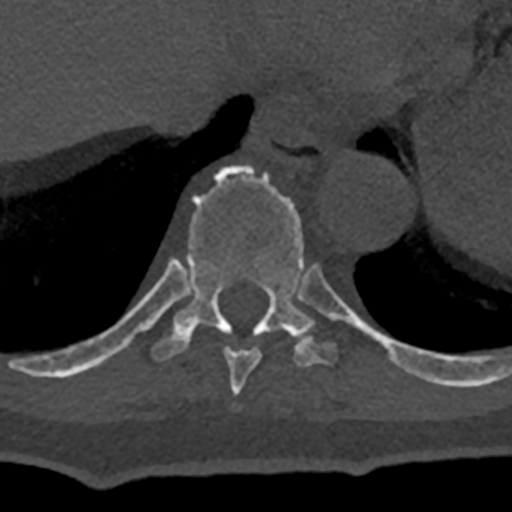
CT including the spine, one axial slice; position 620 of 797 along the scan axis; reconstruction kernel Br40s/3; 120 kVp; bone window (W 1800 / L 400 HU); 512 × 512 image matrix, field of view 160 × 160 mm. Patient: male, 74 years. From the clinical record (not read from this slice): primary cancer: renal.
Structures marked on this image (semi-automatic segmentation, software-assisted and operator-edited):
- T10 vertebra: bounding box <70,165,432,382> (left, top, right, bottom; pixels)
- T9 vertebra: <224,347,262,395>